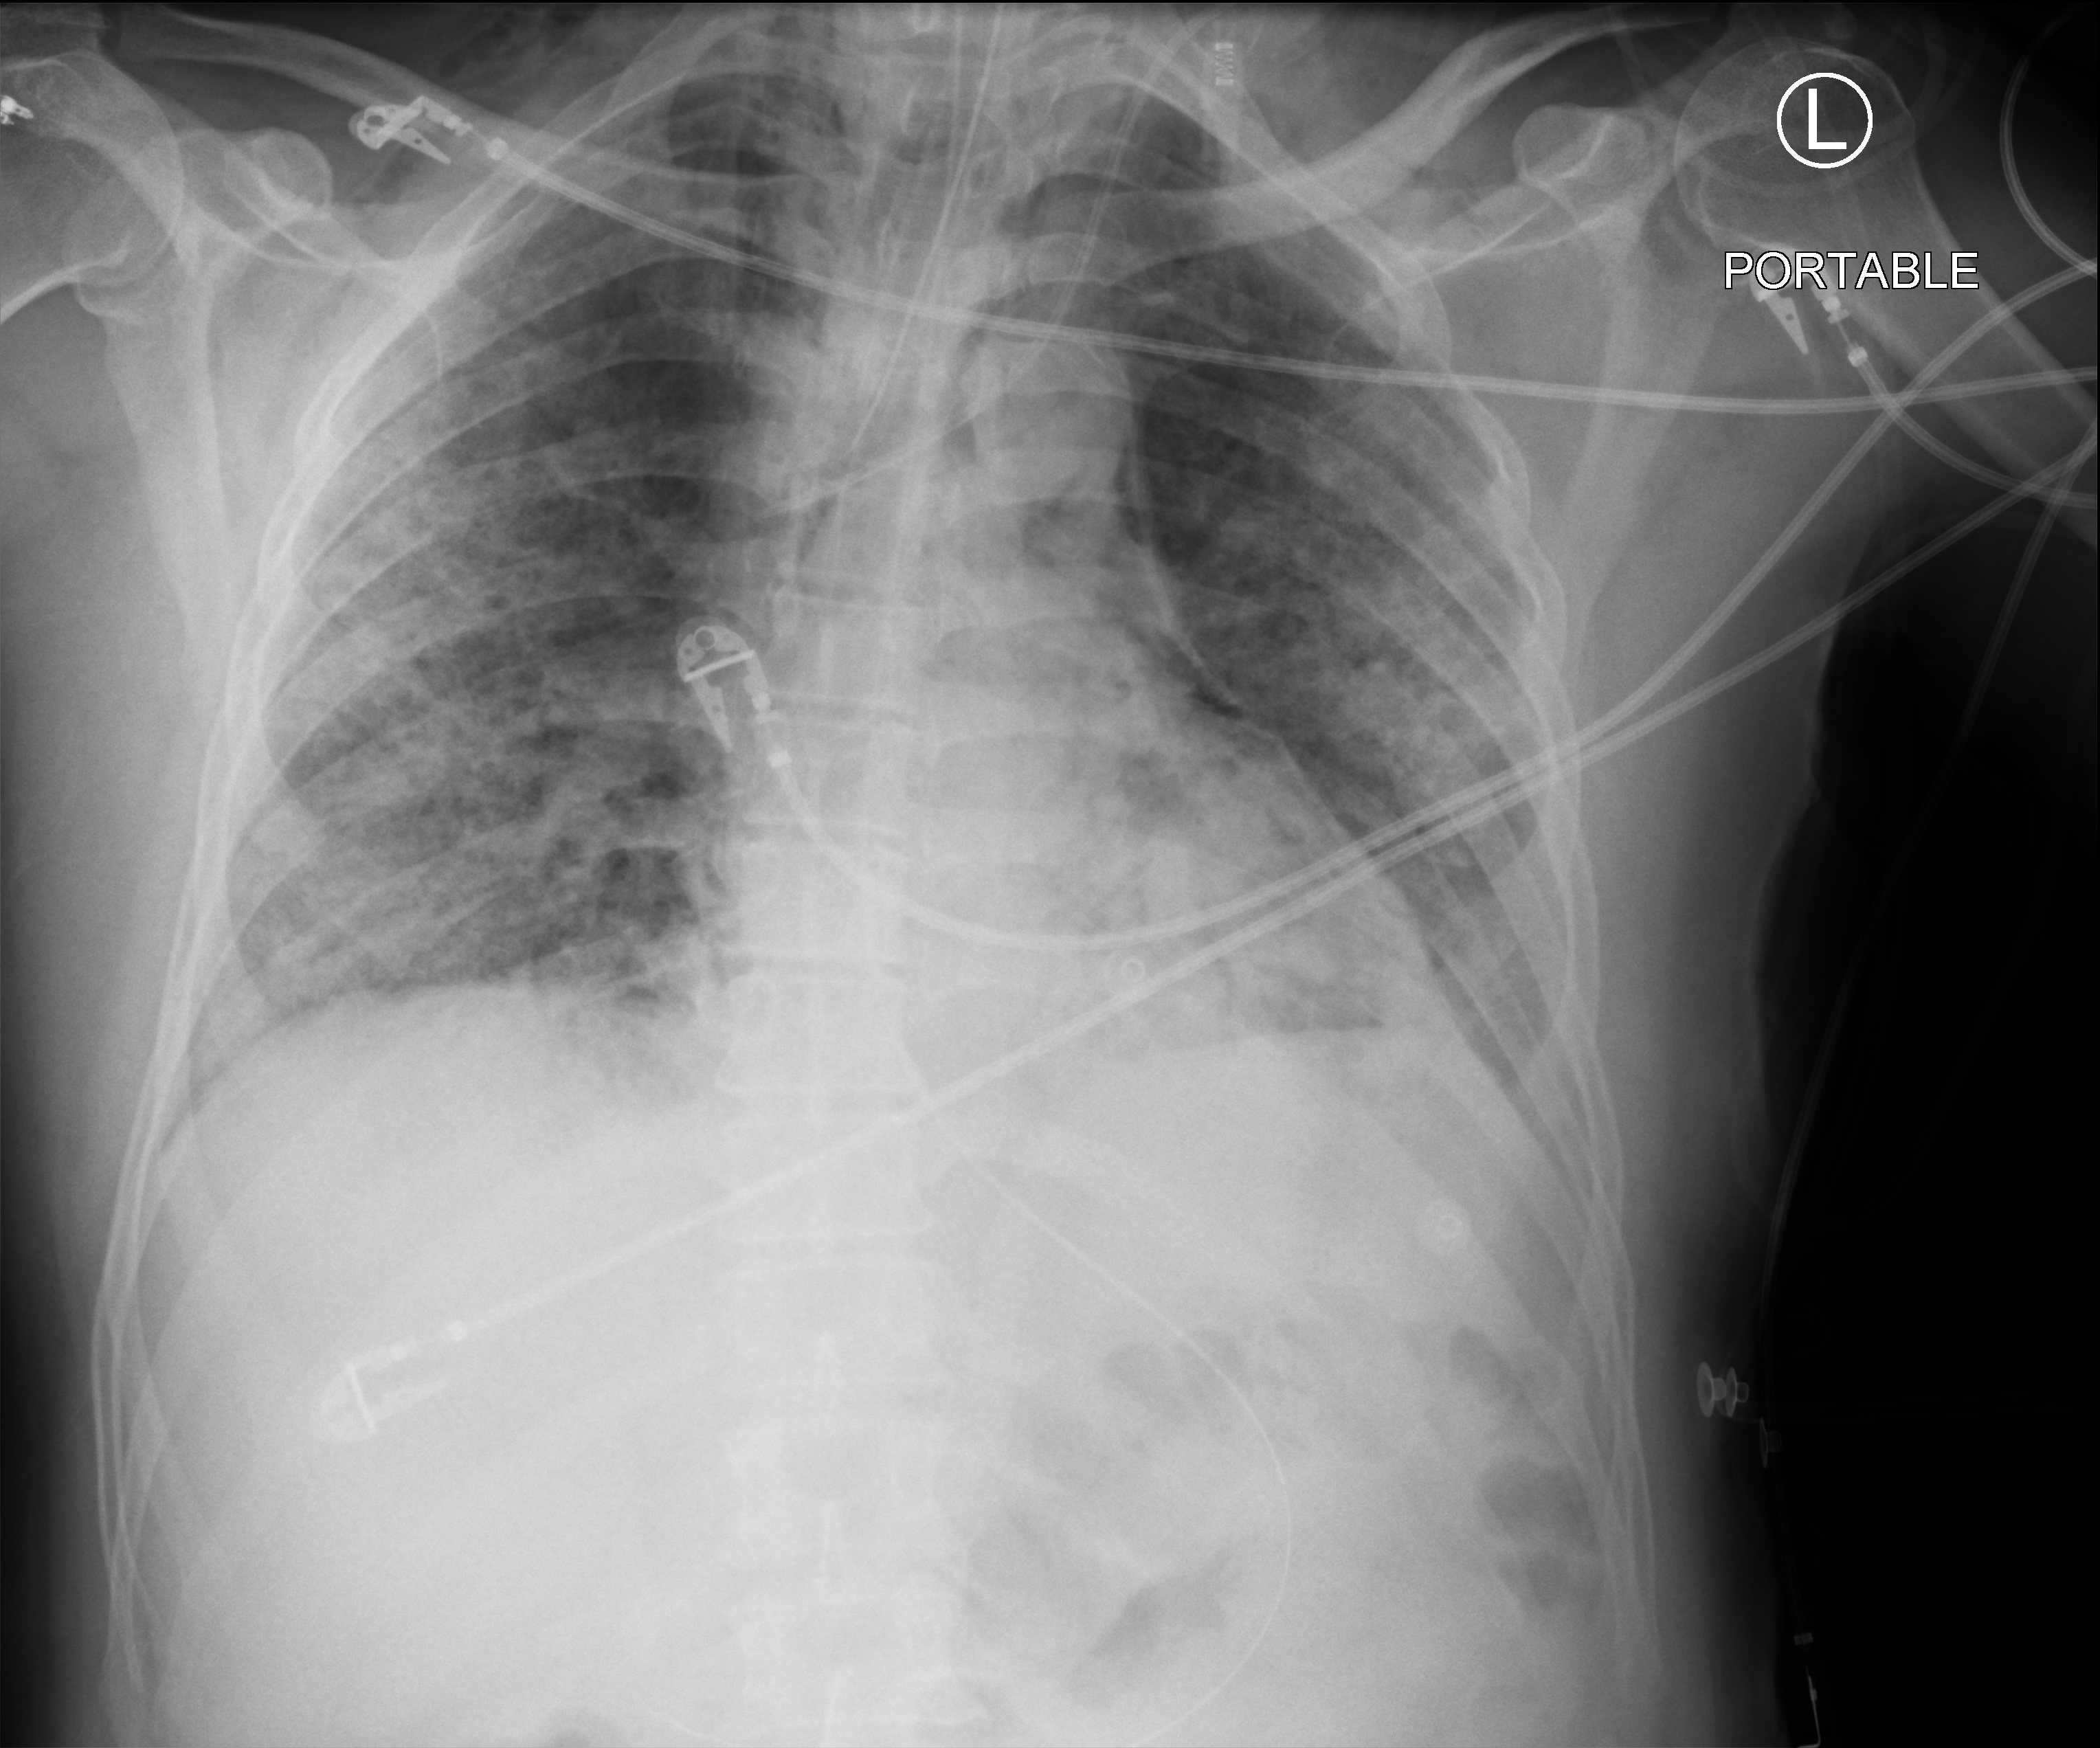
Chest X-ray (portable). Patient hospitalised with COVID-19; male, aged 60–74 years.
From the hospital-stay record, not from the radiograph (when in the stay this image was taken is not recorded): admitted to intensive care during this hospital stay: yes; COPD (admission record): no; mechanically ventilated during this hospital stay: yes.